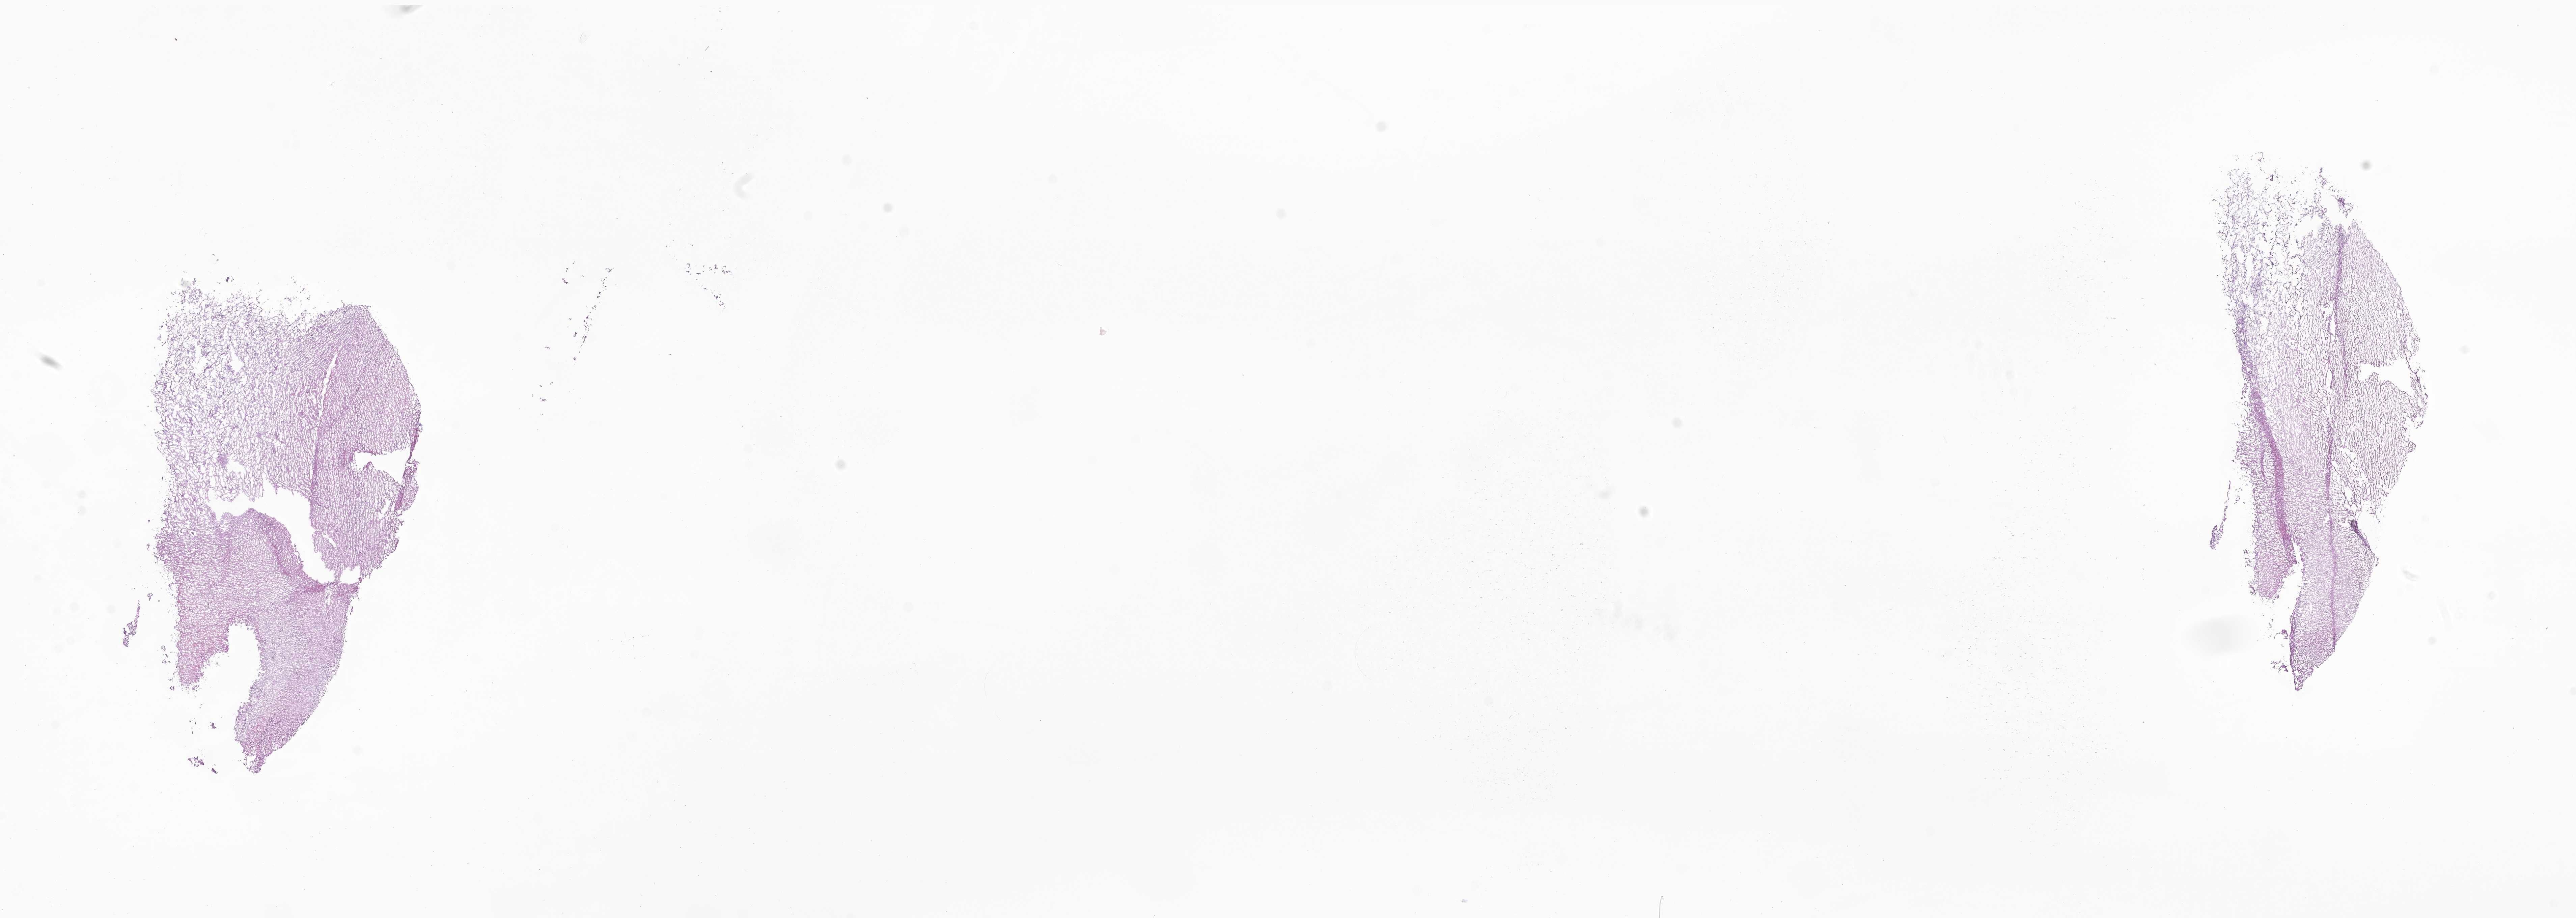
Whole-slide image, H&E stain of tumor tissue from the cerebellum, shown as a low-resolution overview of the whole scanned area (about 32.2 x 11.5 mm); cryosection (OCT / tissue freezing medium). Patient female; age 48 months (4 years).
Diagnosis (ICD-O-3 morphology term): Pilocytic astrocytoma.